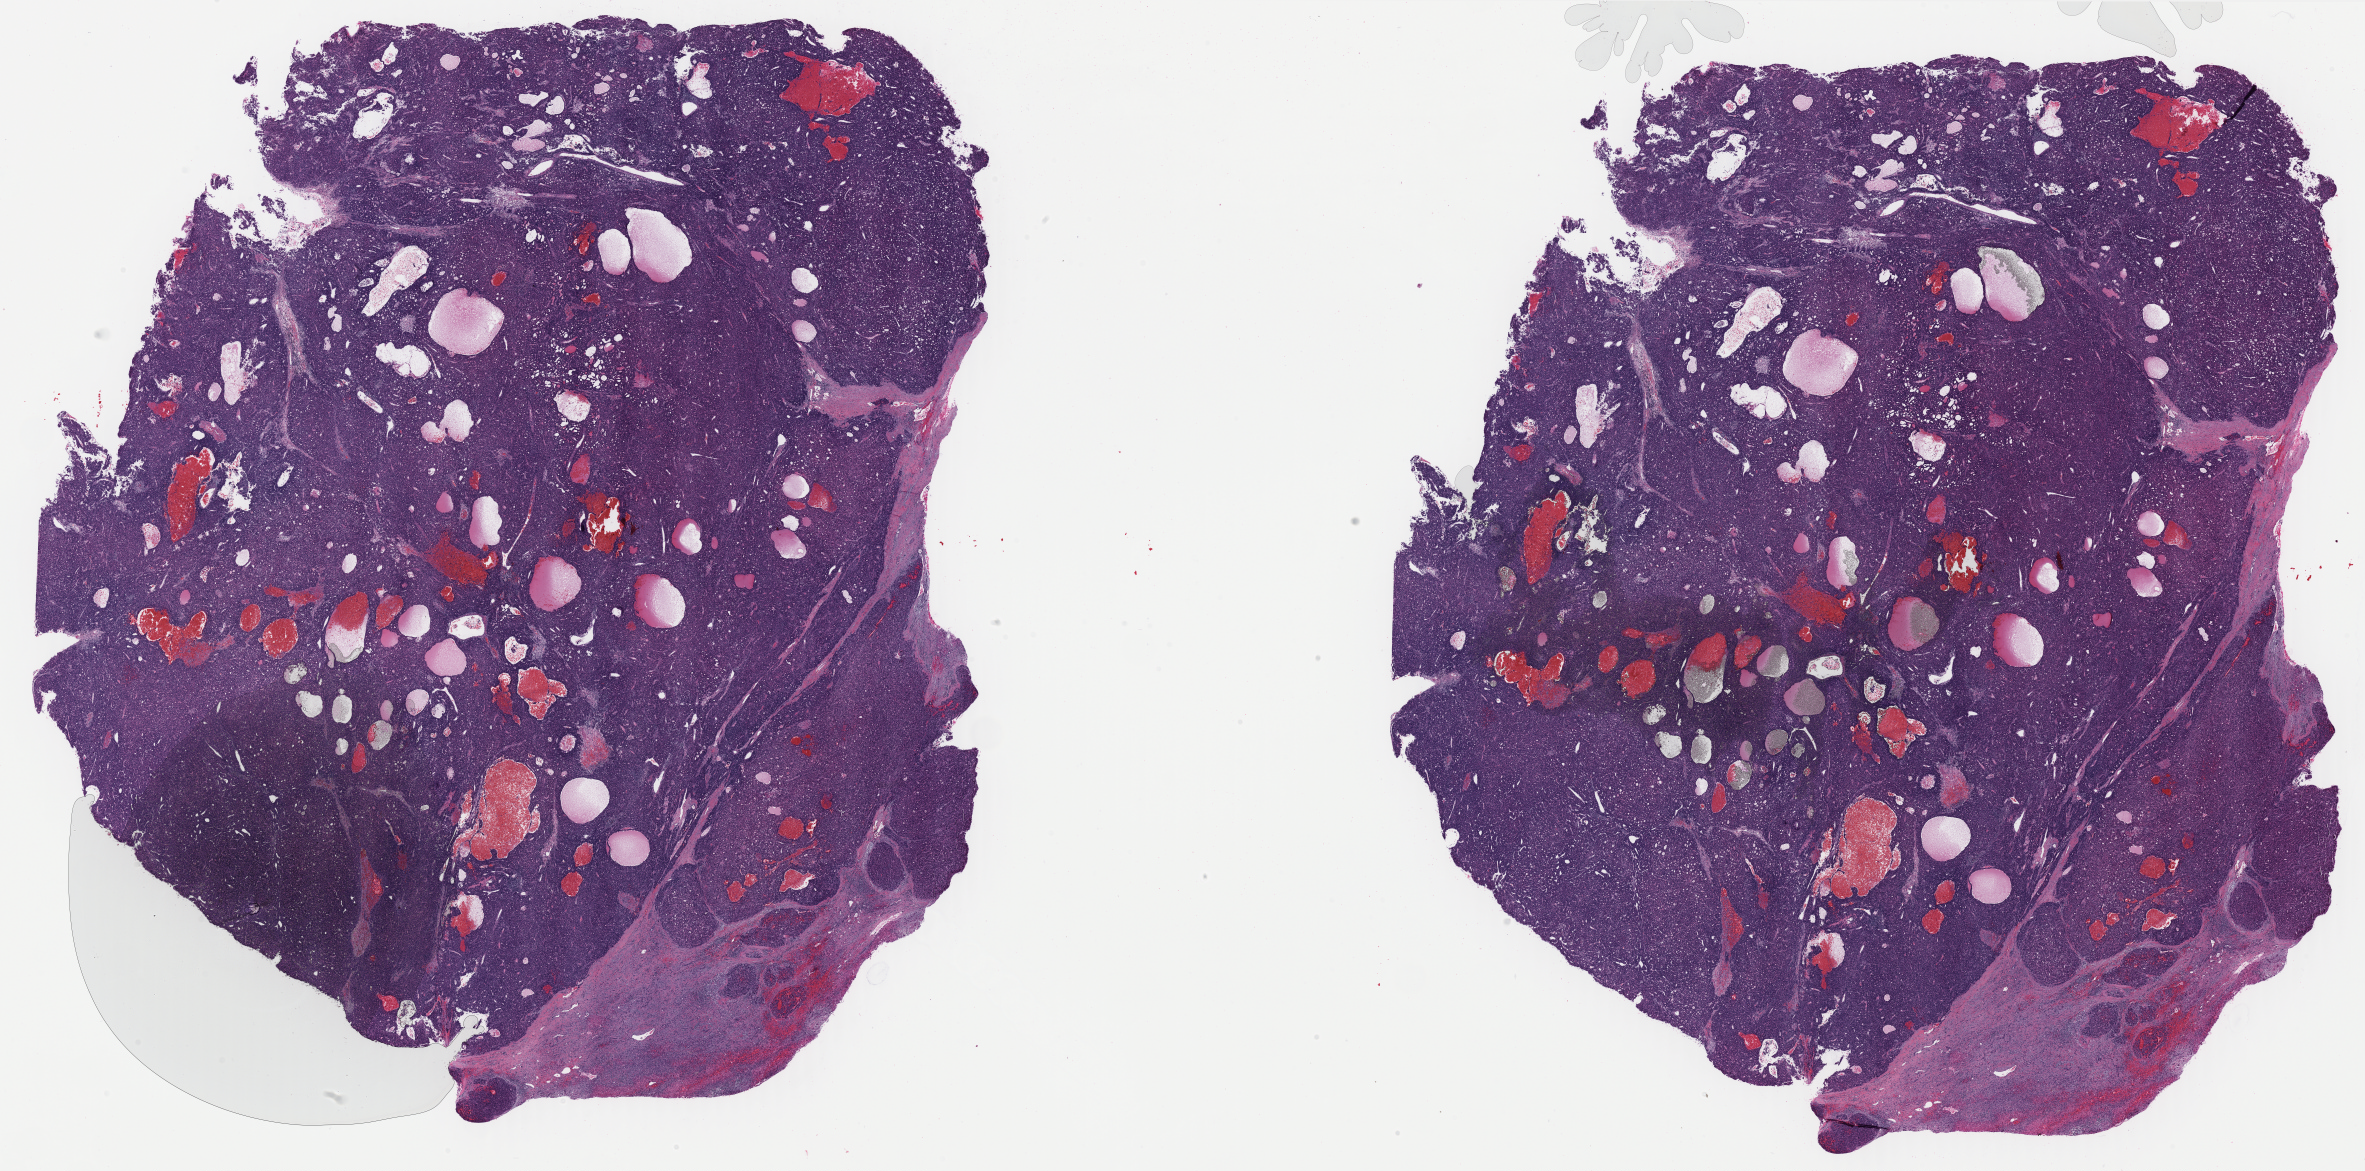
Digitized H&E-stained tissue section (whole slide) — whole scanned area (about 37.4 x 18.5 mm, acquisition: 40x scan) shown as a low-resolution overview, FFPE section, liver, primary tumour sample. Female, age 75 years at initial diagnosis. Histologic grade: G3 (poorly differentiated).
Histologic diagnosis: Hepatocellular carcinoma, NOS. AJCC pathologic stage: II (7th edition).